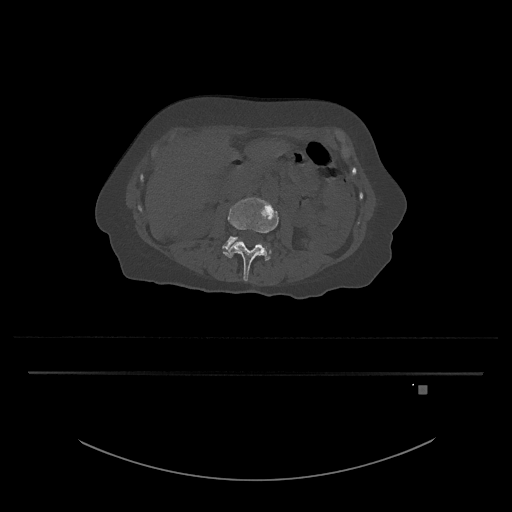
CT including the spine, one axial slice; slice 412 of 797 in the series (ordered by position); reconstruction kernel Br40s/3; bone window (W 1800 / L 400 HU); 0.5 mm slice thickness; 512 × 512 image matrix, field of view 500 × 500 mm. Female patient, age 57 years. Case-level facts recorded for this patient, not image findings: primary cancer: cervical.
Outlined on this slice (semi-automatic segmentation, software-assisted and operator-edited):
- L3 vertebra: bounding box (x1, y1, x2, y2) in pixels: (223, 198, 279, 281)
- L4 vertebra: (222, 236, 271, 261)